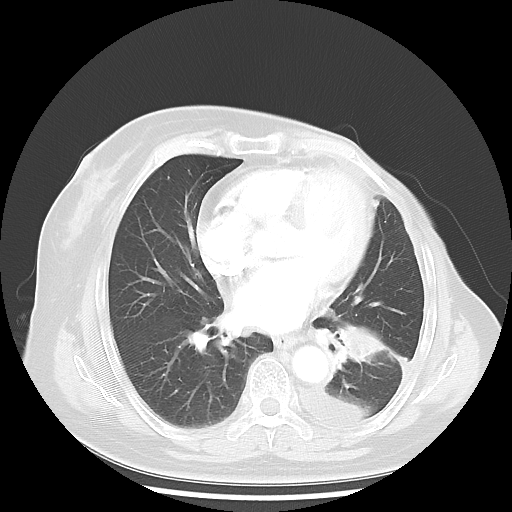
Chest CT, one axial slice; slice 20 of 48 in the series (ordered by position); reconstruction kernel LUNG; lung window (W 1500 / L -600 HU); 5 mm slice thickness; 512 × 512 image matrix, field of view 360 × 360 mm. Patient: female, 63 years. Case-level facts recorded for this patient, not image findings: clinical TNM (as recorded): T2 N0 M1.
Structures marked on this image (bounding box drawn by a radiologist):
- lung tumour (recorded histology: adenocarcinoma): bounding box (x1, y1, x2, y2) in pixels: (329, 317, 391, 366)